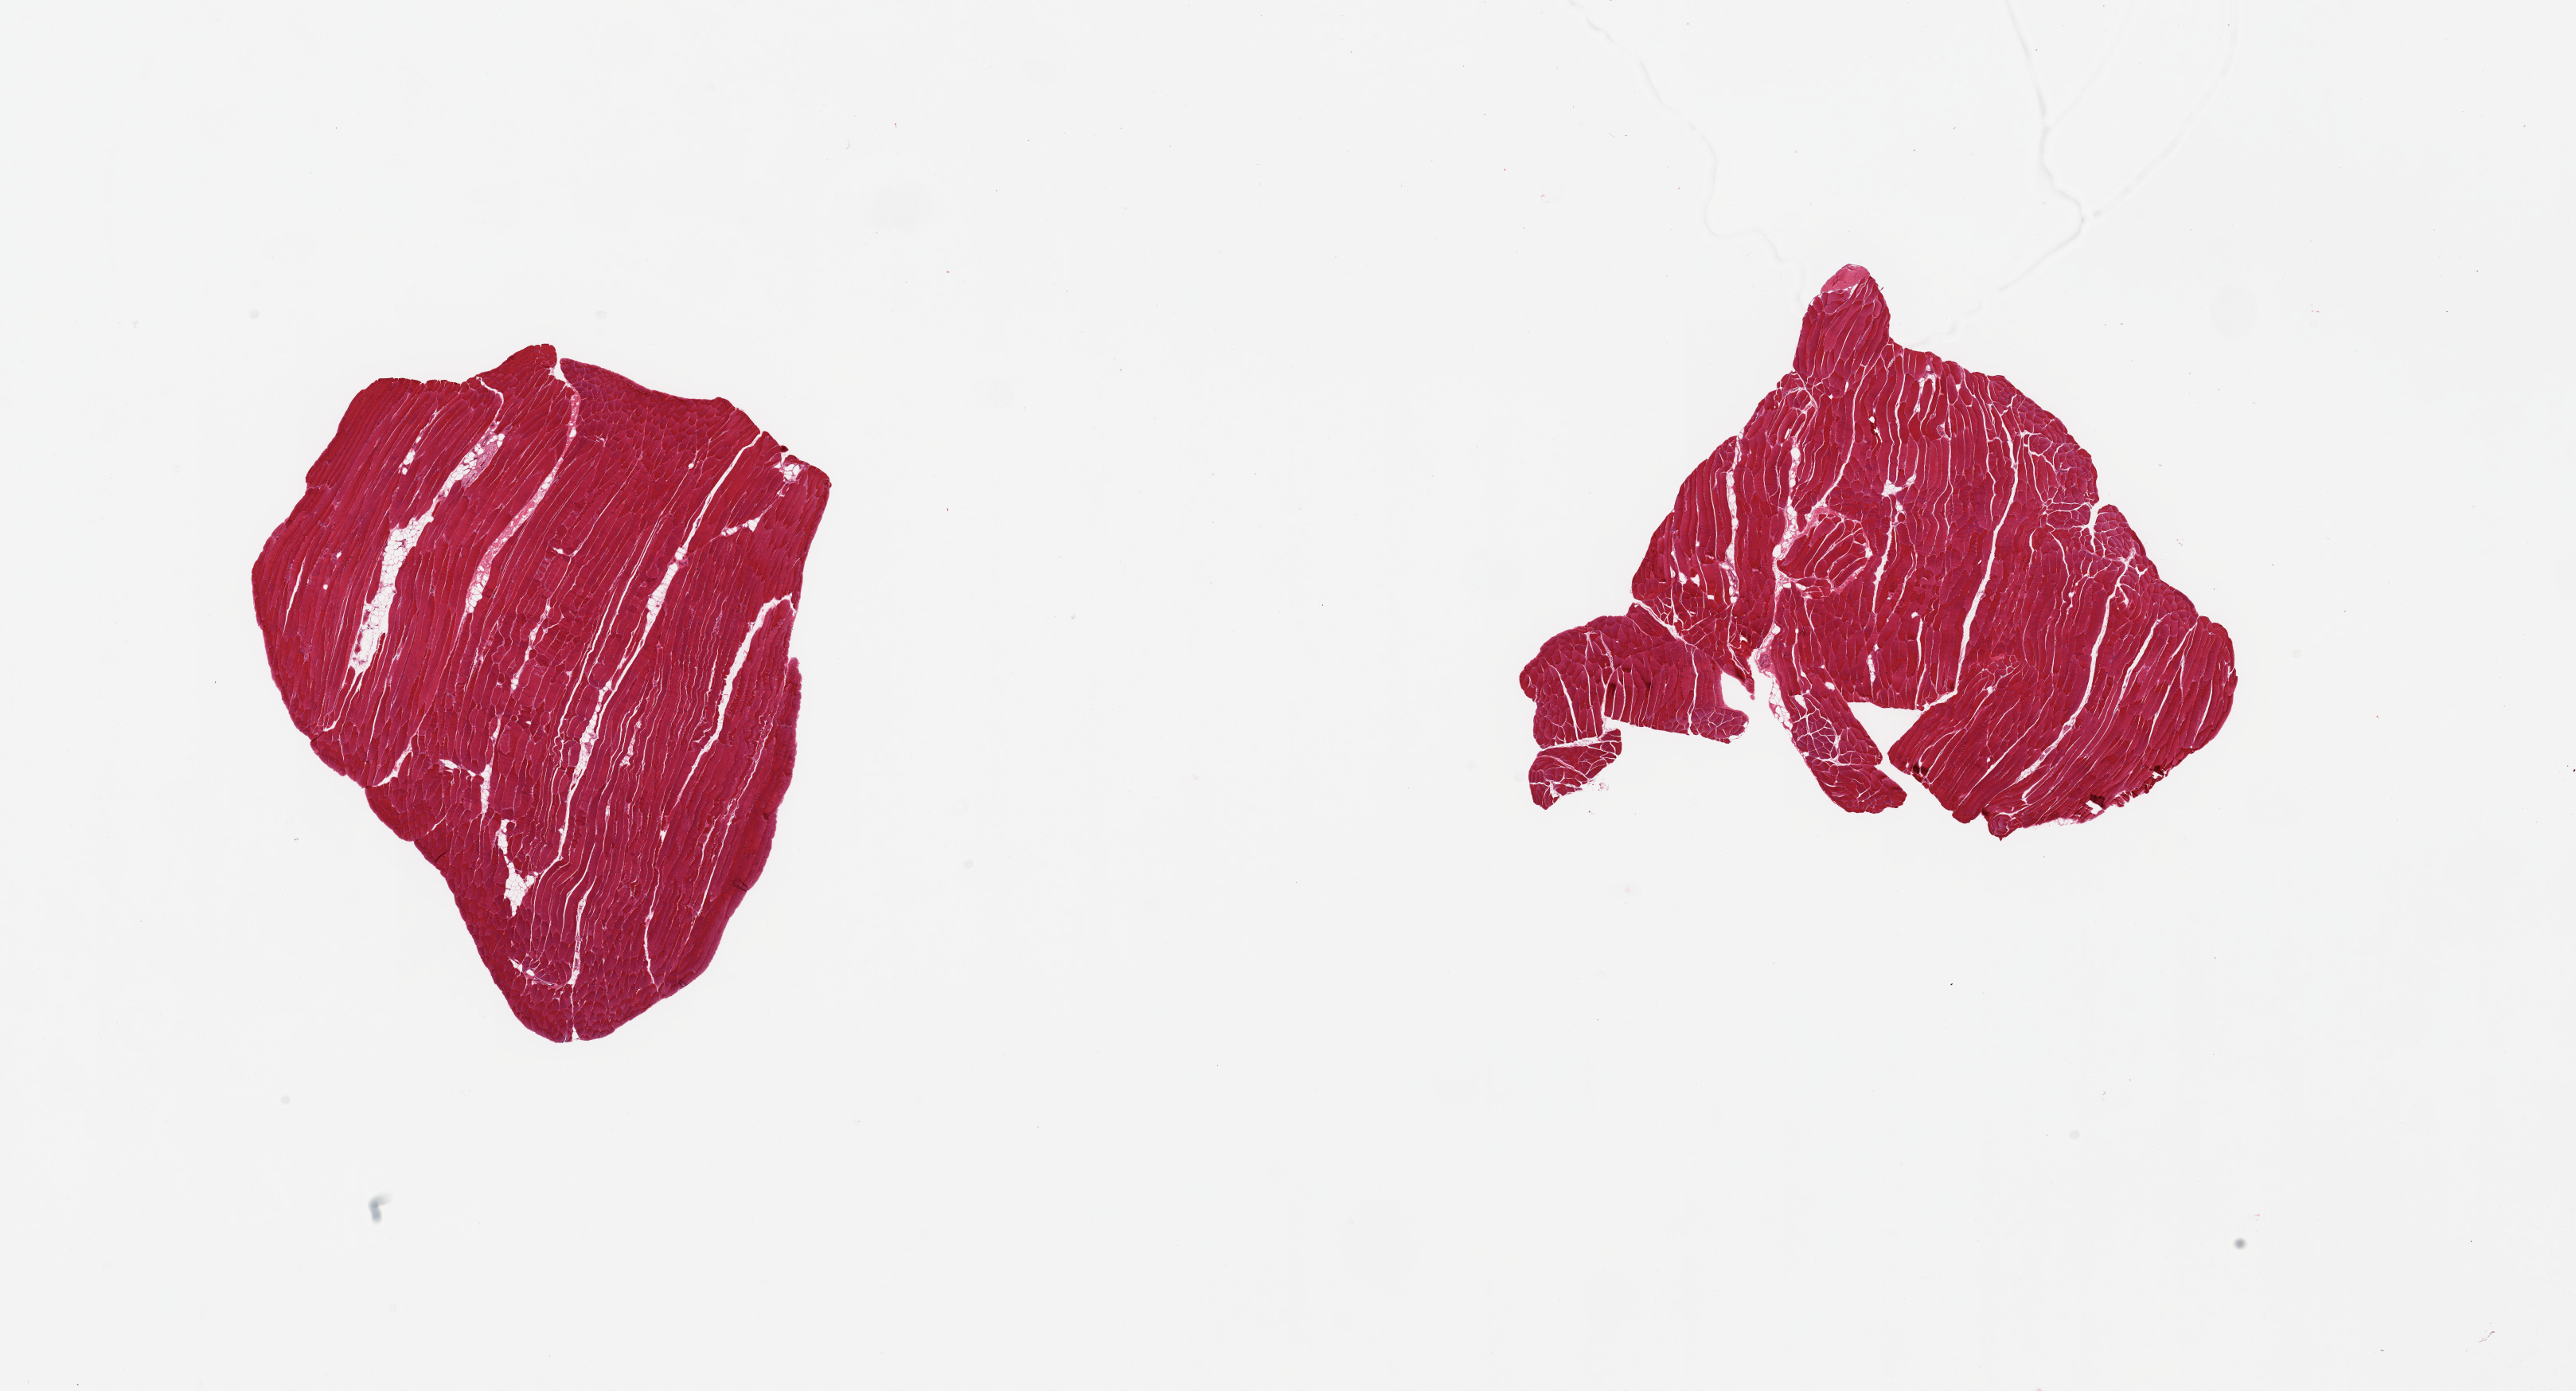
Digitized H&E-stained section, brightfield — low-resolution overview of the scanned area, about 25.6 x 13.8 mm (from a 20x scan); PAXgene-fixed, paraffin-embedded tissue; sampled site (target tissue): skeletal muscle; tissue donor sample. Female donor.
Pathologist's review note for this sample: 2 pieces, minimal interstitial fat.